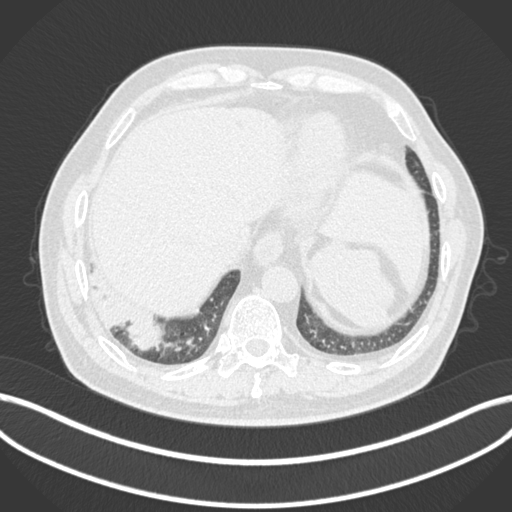
Chest CT, one axial slice. Position 20 of 200 along the scan axis. 120 kVp. Lung window (W 1500 / L -600 HU). 1 mm slice thickness. 512 × 512 image matrix, field of view 400 × 400 mm. Male patient, age 59 years.
Outlined on this slice (bounding box drawn by a radiologist):
- lung tumour (recorded histology: adenocarcinoma): box from (x=87, y=274) to (x=167, y=355) px